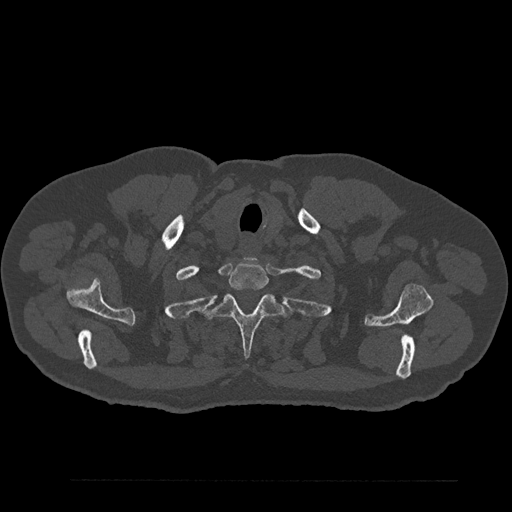
CT including the spine, one axial slice; slice 729 of 797 in the series (ordered by position); 120 kVp; bone window (W 1800 / L 400 HU); 0.5 mm slice thickness; 512 × 512 image matrix. Male patient, age 61 years. From the clinical record (not read from this slice): primary cancer: prostate.
Annotated regions visible in this slice (semi-automatic segmentation, software-assisted and operator-edited):
- T1 vertebra: bounding box <228,262,269,291> (left, top, right, bottom; pixels)
- T2 vertebra: <209,294,290,357>